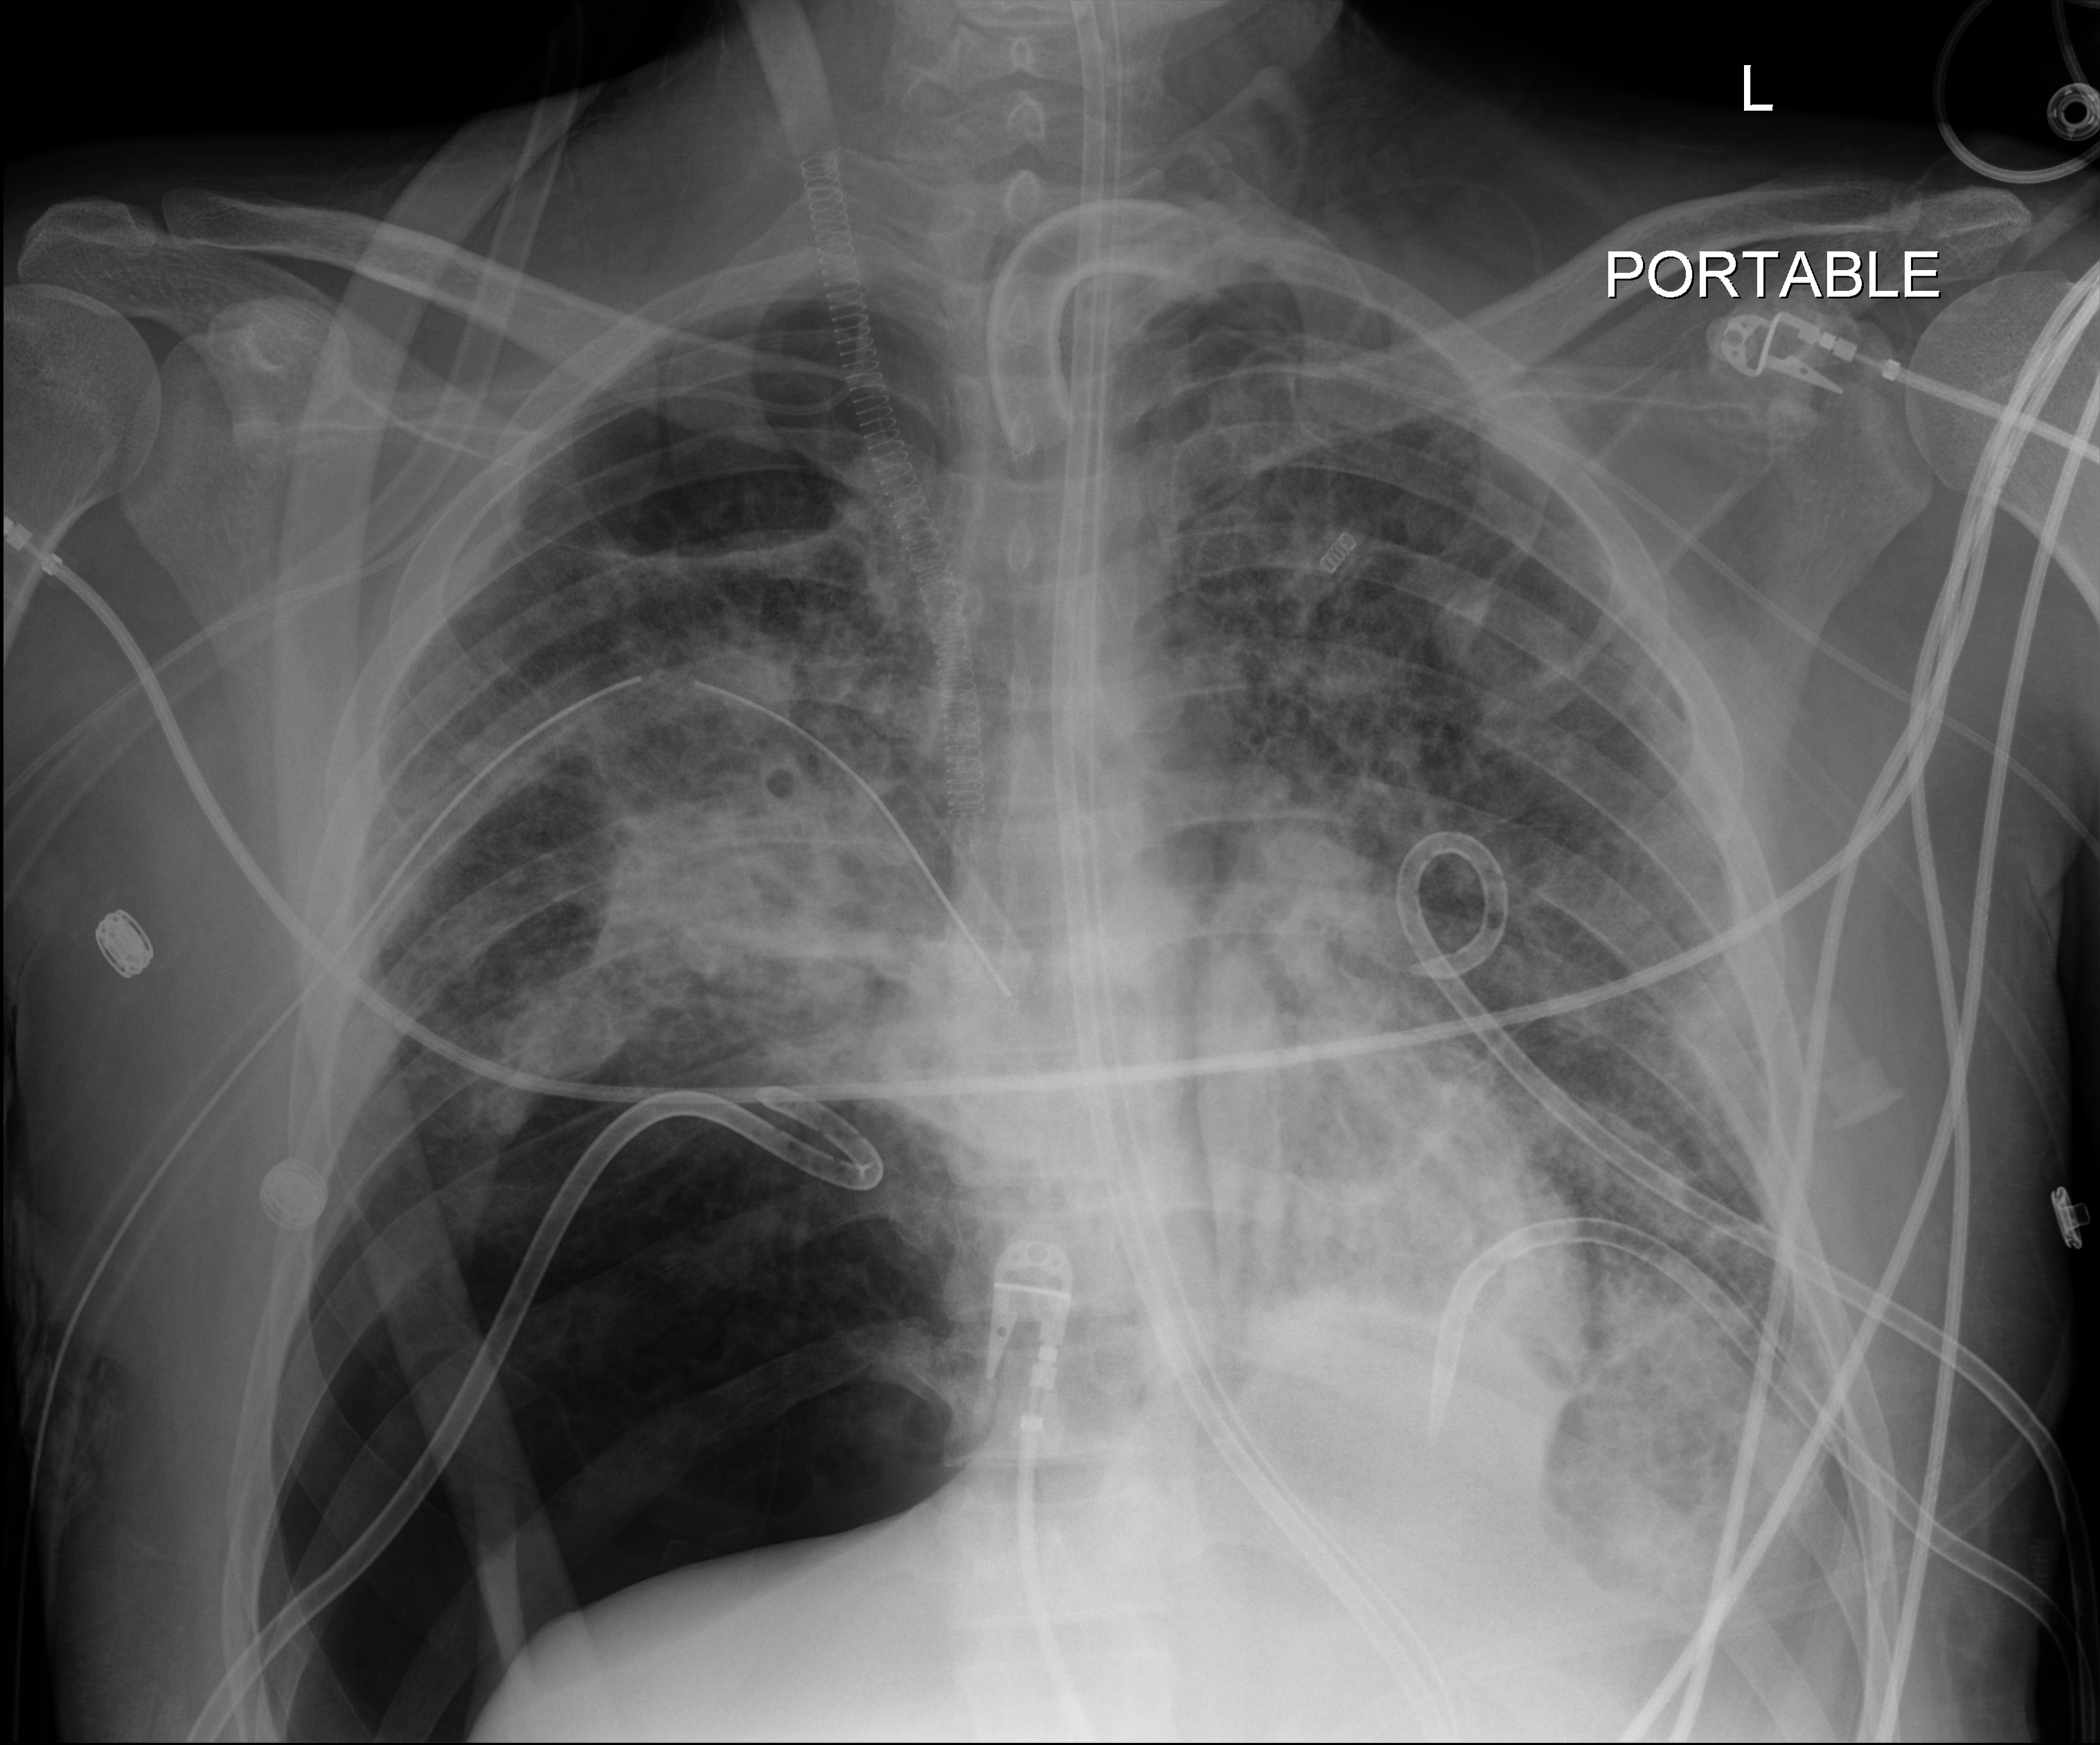
Bedside chest radiograph (digital radiography), anteroposterior (AP) projection. Patient hospitalised with COVID-19, aged 18–59 years.
From the hospital-stay record, not from the radiograph (when in the stay this image was taken is not recorded): COPD (admission record): no; mechanically ventilated during this hospital stay: yes; diabetes (admission record): no.